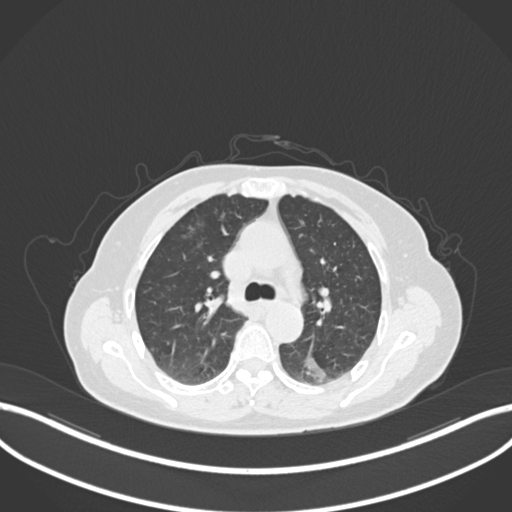
Chest CT, one axial slice. Reconstruction kernel B30f. Lung window (W 1500 / L -600 HU). 1 mm slice thickness. 512 × 512 image matrix, field of view 400 × 400 mm. Patient: female, 70 years. Case-level facts recorded for this patient, not image findings: clinical TNM (as recorded): T1c N0 M0.
Outlined on this slice (bounding box drawn by a radiologist):
- lung tumour (recorded histology: adenocarcinoma): bounding box <303,353,332,389> (left, top, right, bottom; pixels)